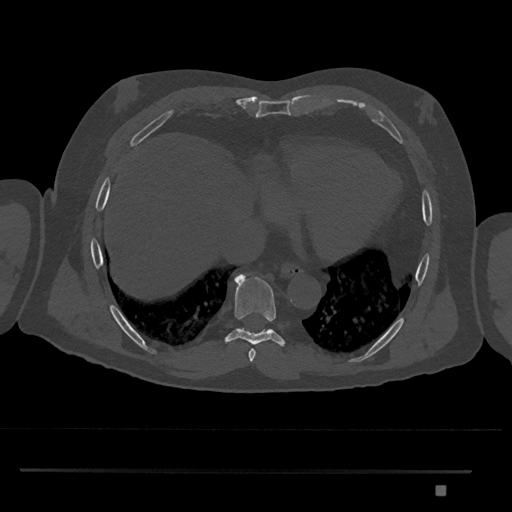
CT including the spine, one axial slice. Slice 1109 of 1134 in the series (ordered by position). Reconstruction kernel Br40s/3. Bone window (W 1800 / L 400 HU). 0.5 mm slice thickness. 512 × 512 image matrix, field of view 429 × 429 mm. Patient: male, 65 years. Case-level facts recorded for this patient, not image findings: primary cancer: prostate.
Outlined on this slice (semi-automatic segmentation, software-assisted and operator-edited):
- T8 vertebra: box from (x=225, y=274) to (x=285, y=346) px